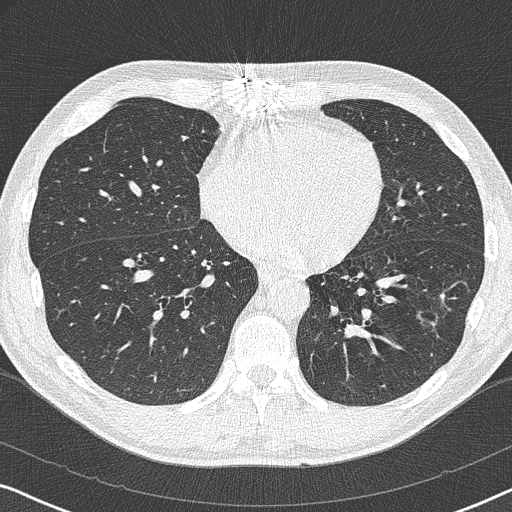
Axial slice from a low-dose chest CT screening exam. Baseline annual screen. Lung window (W 1500 / L -600 HU). 1 mm slice thickness. 120 kVp. Slice 212 of 327 in the series. Male participant, aged 59 years at enrolment. Current smoker at enrolment.
Lesion marked by an expert reader, box from (x=408, y=303) to (x=449, y=334) px. The screening reader recorded 2 non-calcified nodules or masses ≥4 mm on this exam (left lower lobe, right middle lobe); which of them this box marks is not recorded. Official screen result: positive, change unspecified: nodule(s) >= 4 mm or enlarging nodule(s), mass(es), or other non-specific abnormalities suspicious for lung cancer.